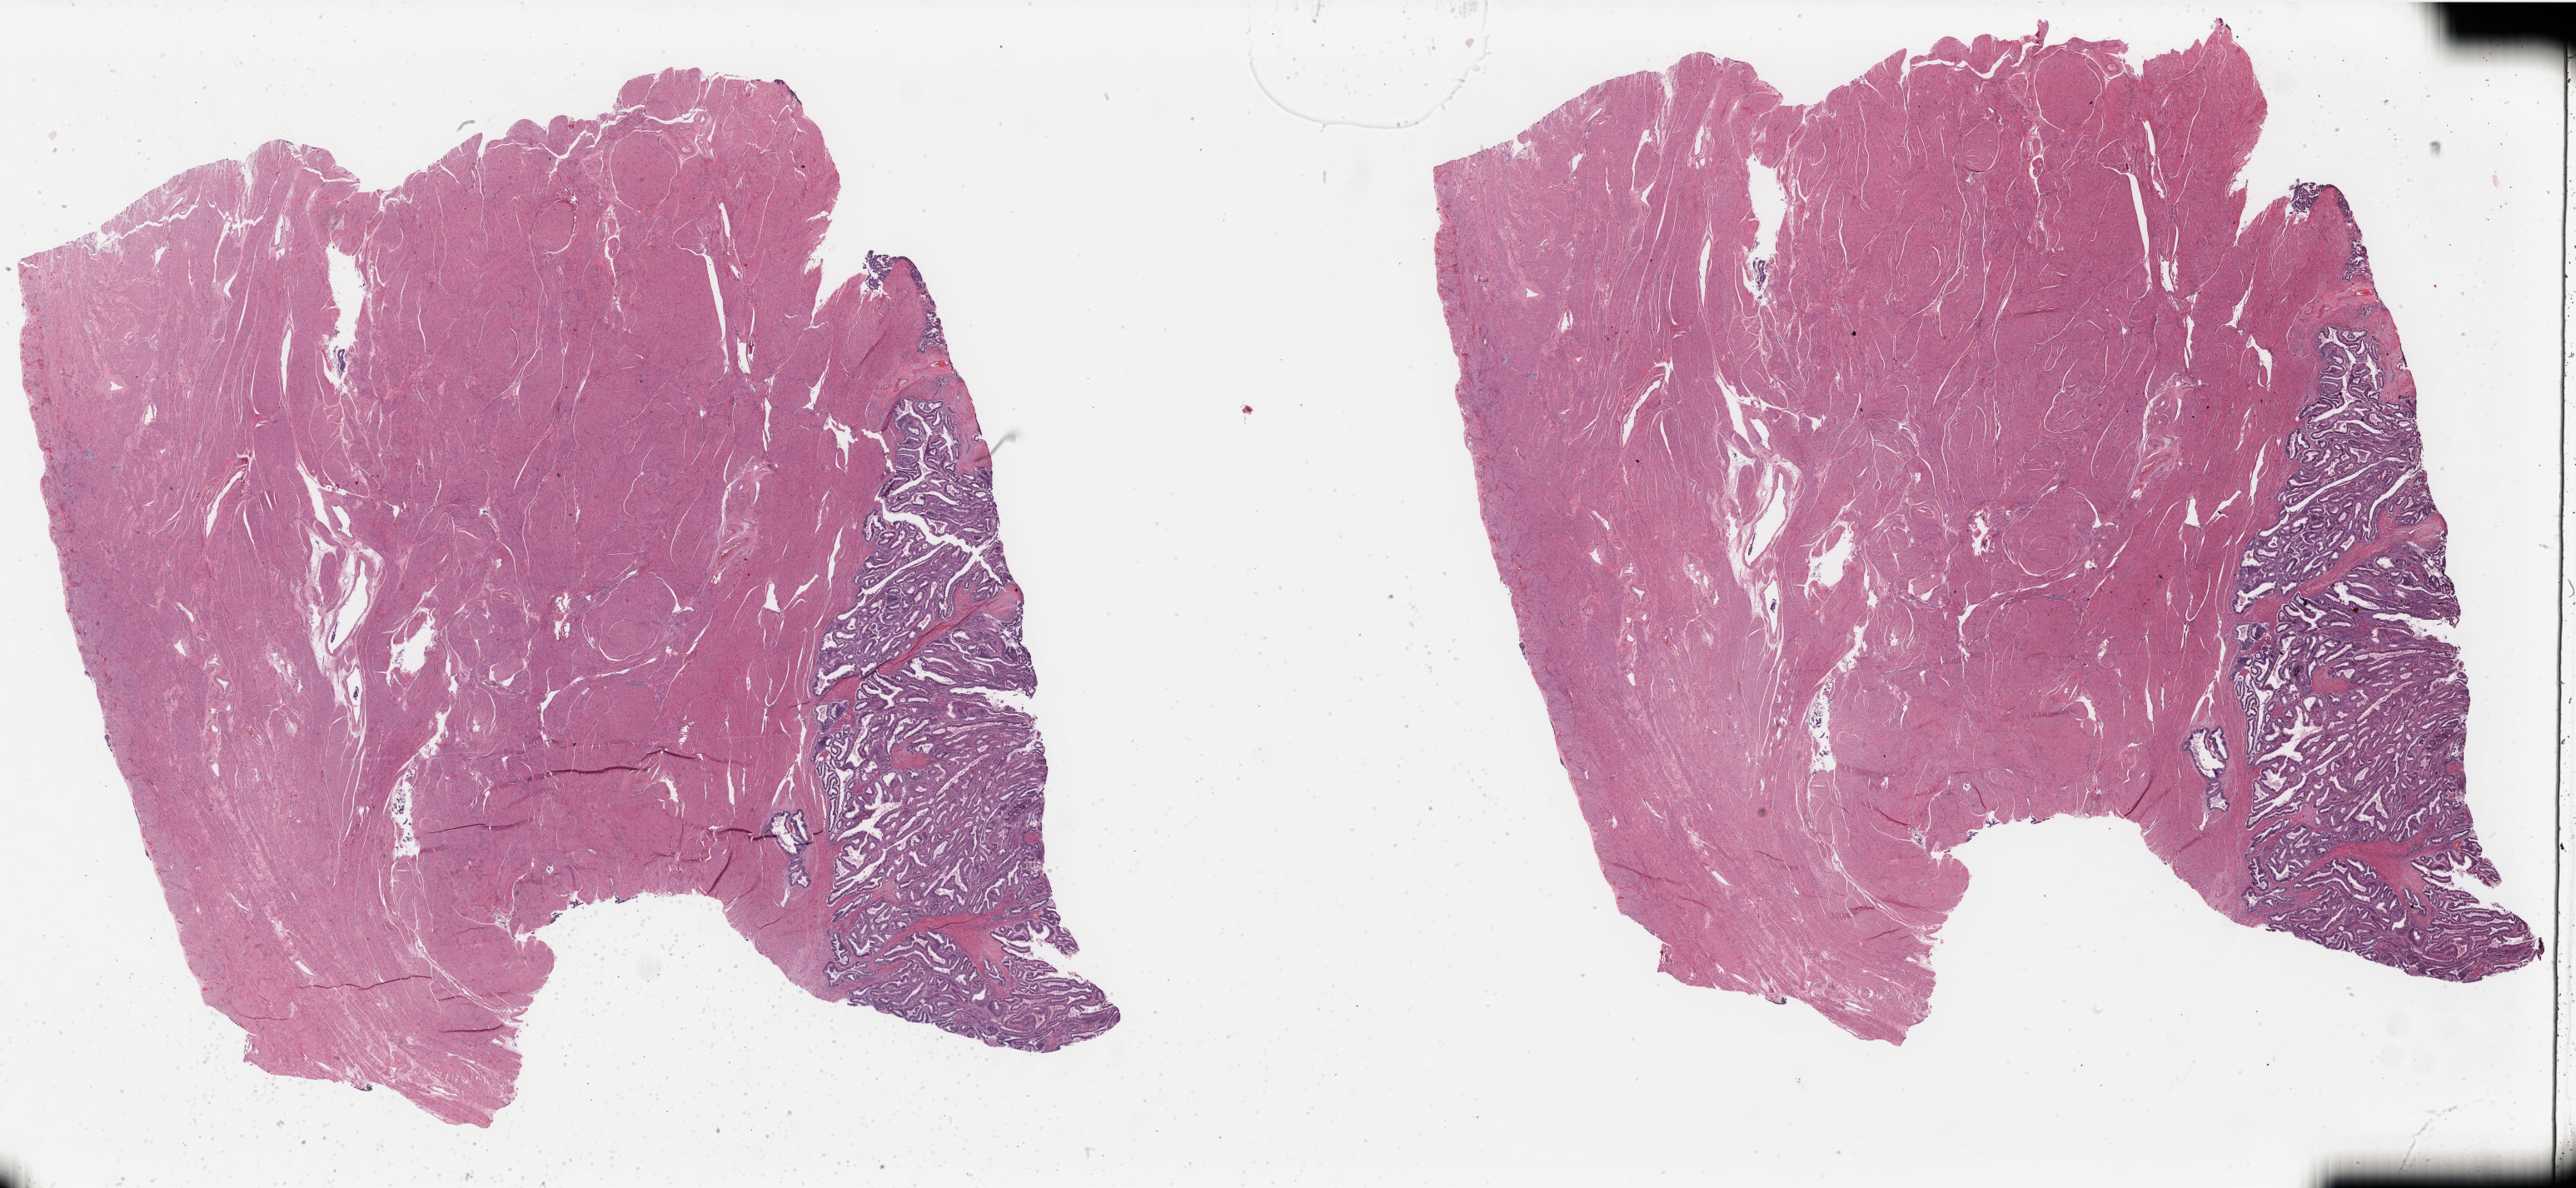
H&E whole-slide image, whole scanned area (about 49.1 x 22.6 mm) shown as a low-resolution overview; FFPE section; uterus, primary tumour sample. Patient: female, age at initial diagnosis 55 years. Histologic grade: G2 (moderately differentiated).
FIGO stage: IA. Diagnosis: Endometrioid adenocarcinoma, NOS (endometrium).